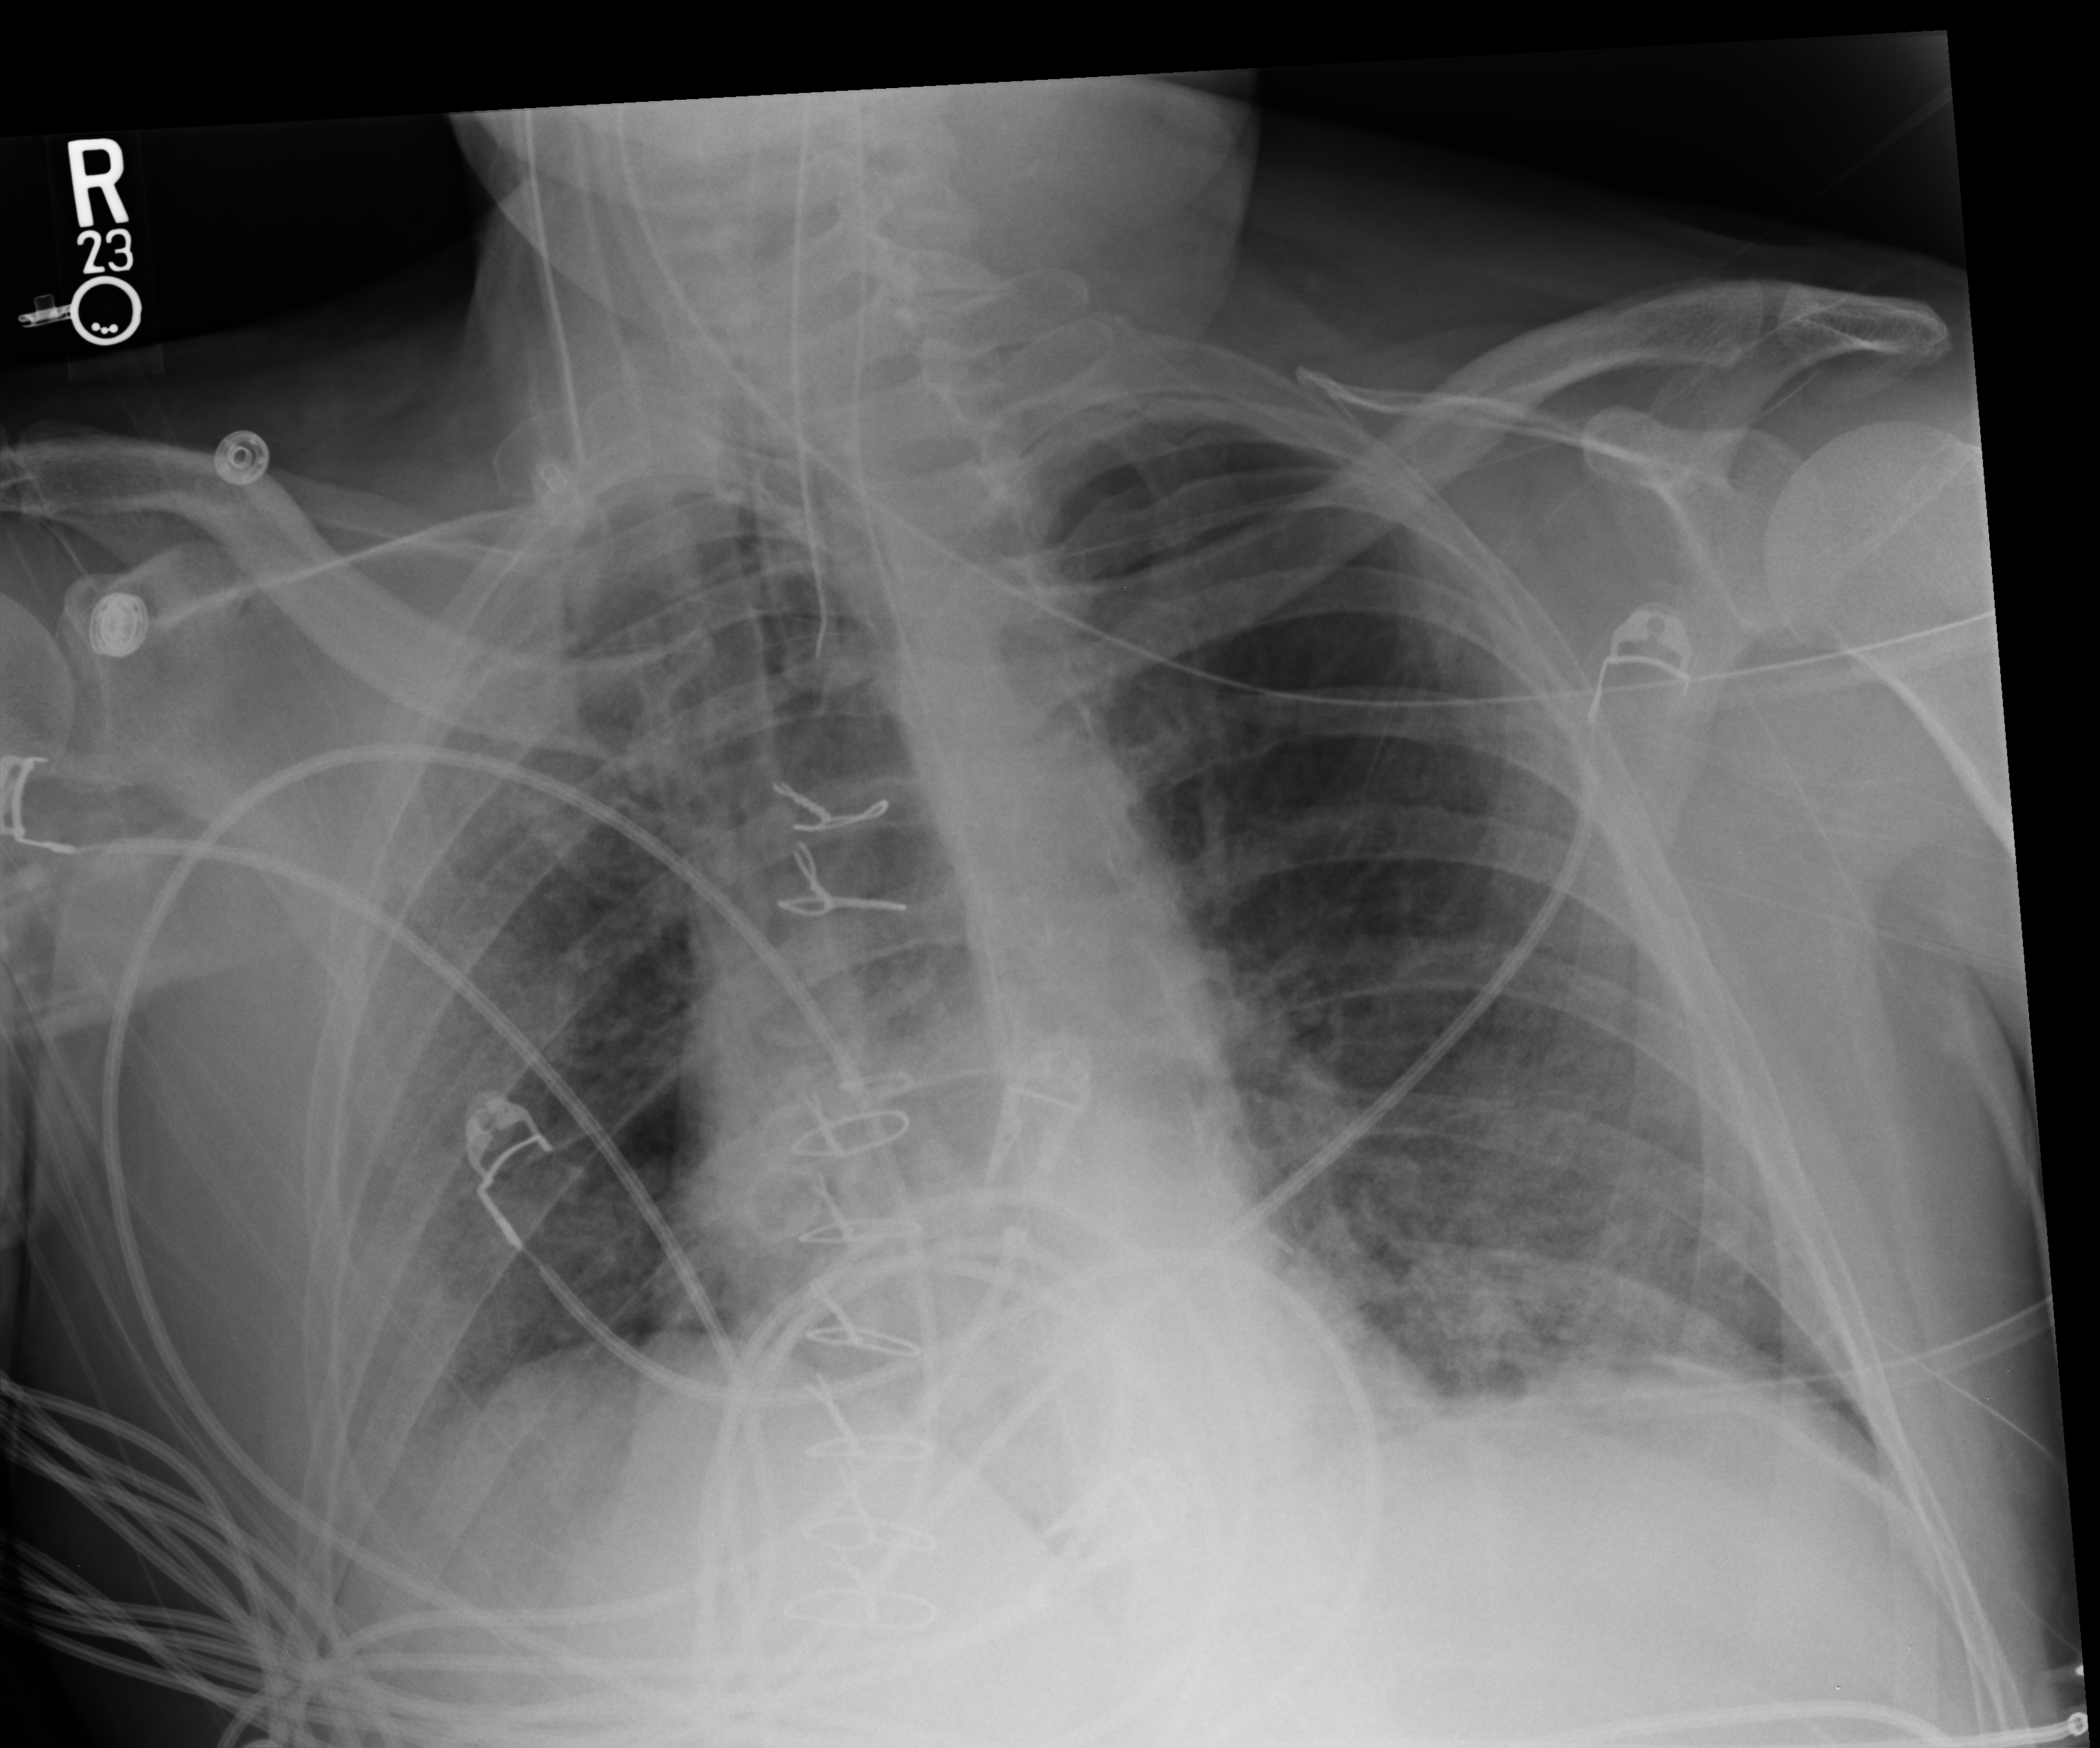
Portable chest radiograph, anteroposterior (AP) projection. Patient hospitalised with COVID-19; male, aged 18–59 years.
Hospital-stay facts (about this admission, not read from this image; timing relative to this image not recorded): admitted to intensive care during this hospital stay: yes.